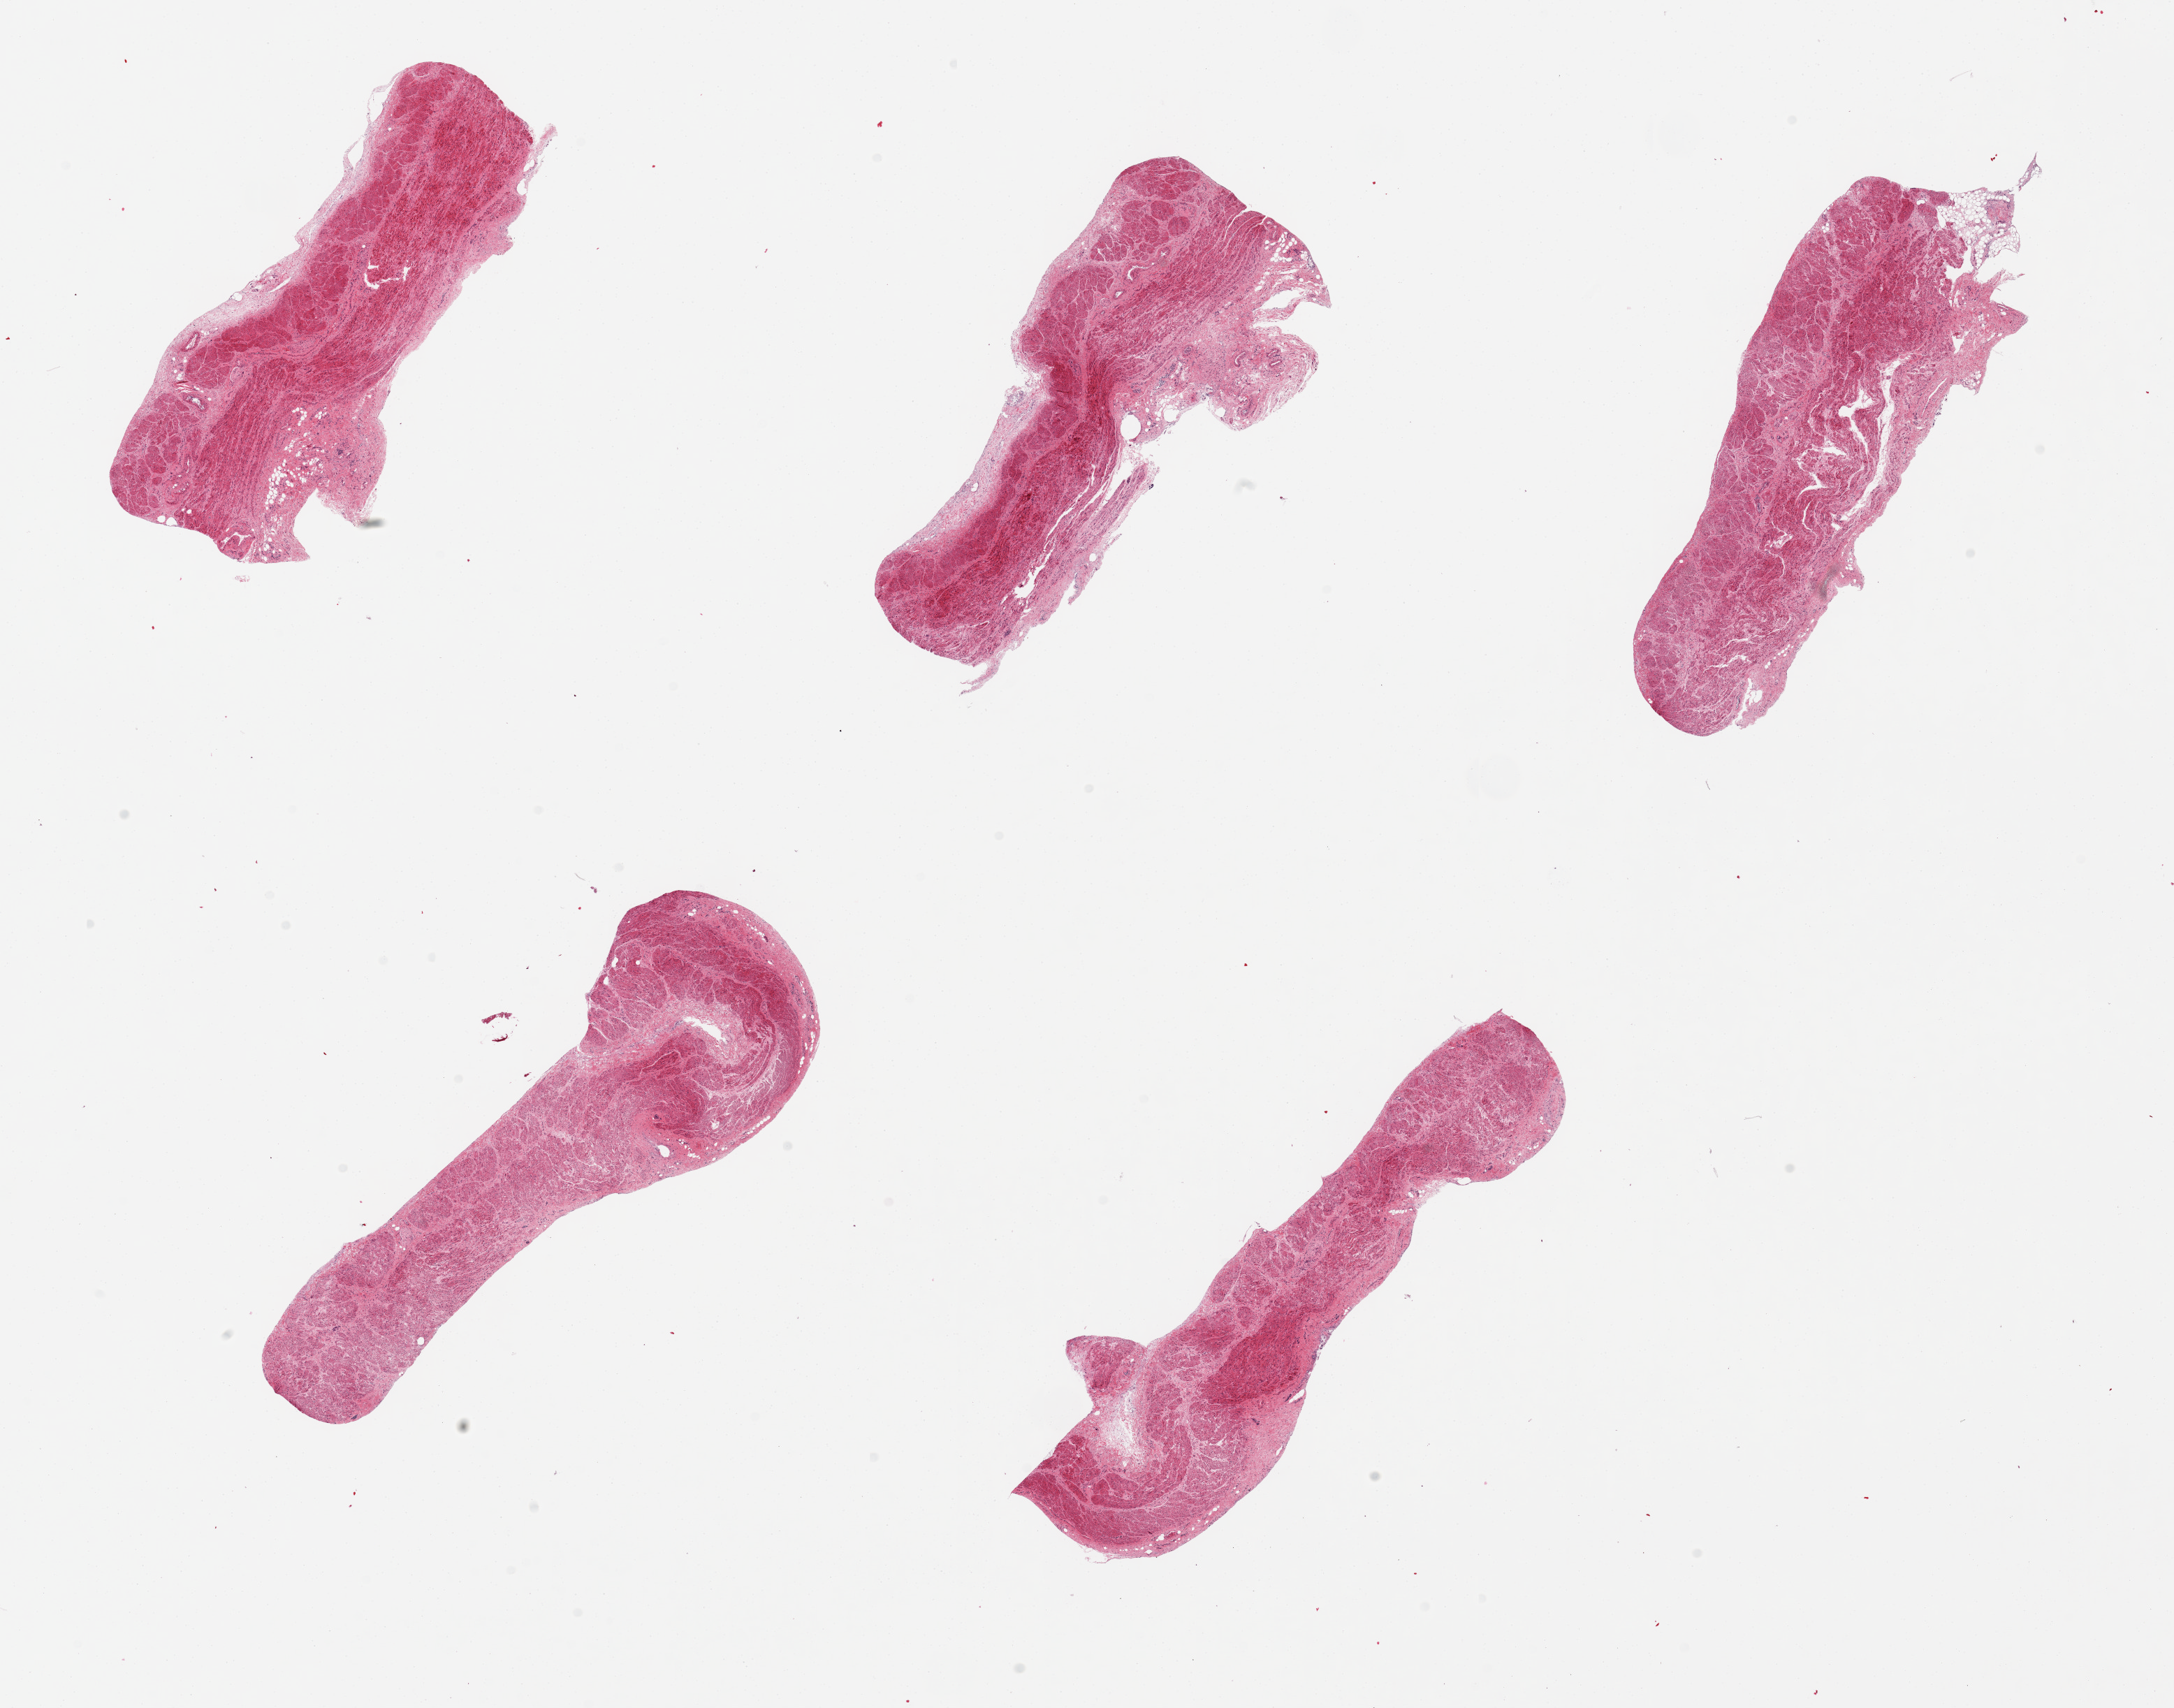
Whole-slide image, hematoxylin and eosin (H&E) stain, low-resolution overview of the scanned area, about 24.6 x 19.3 mm; PAXgene-fixed, paraffin-embedded tissue; sampled site (target tissue): gastroesophageal junction; donor tissue sample. Donor: male.
• reviewer comment on this tissue sample: 6 pieces, mixed smooth muscle and fibroconnective tissue, intermingled